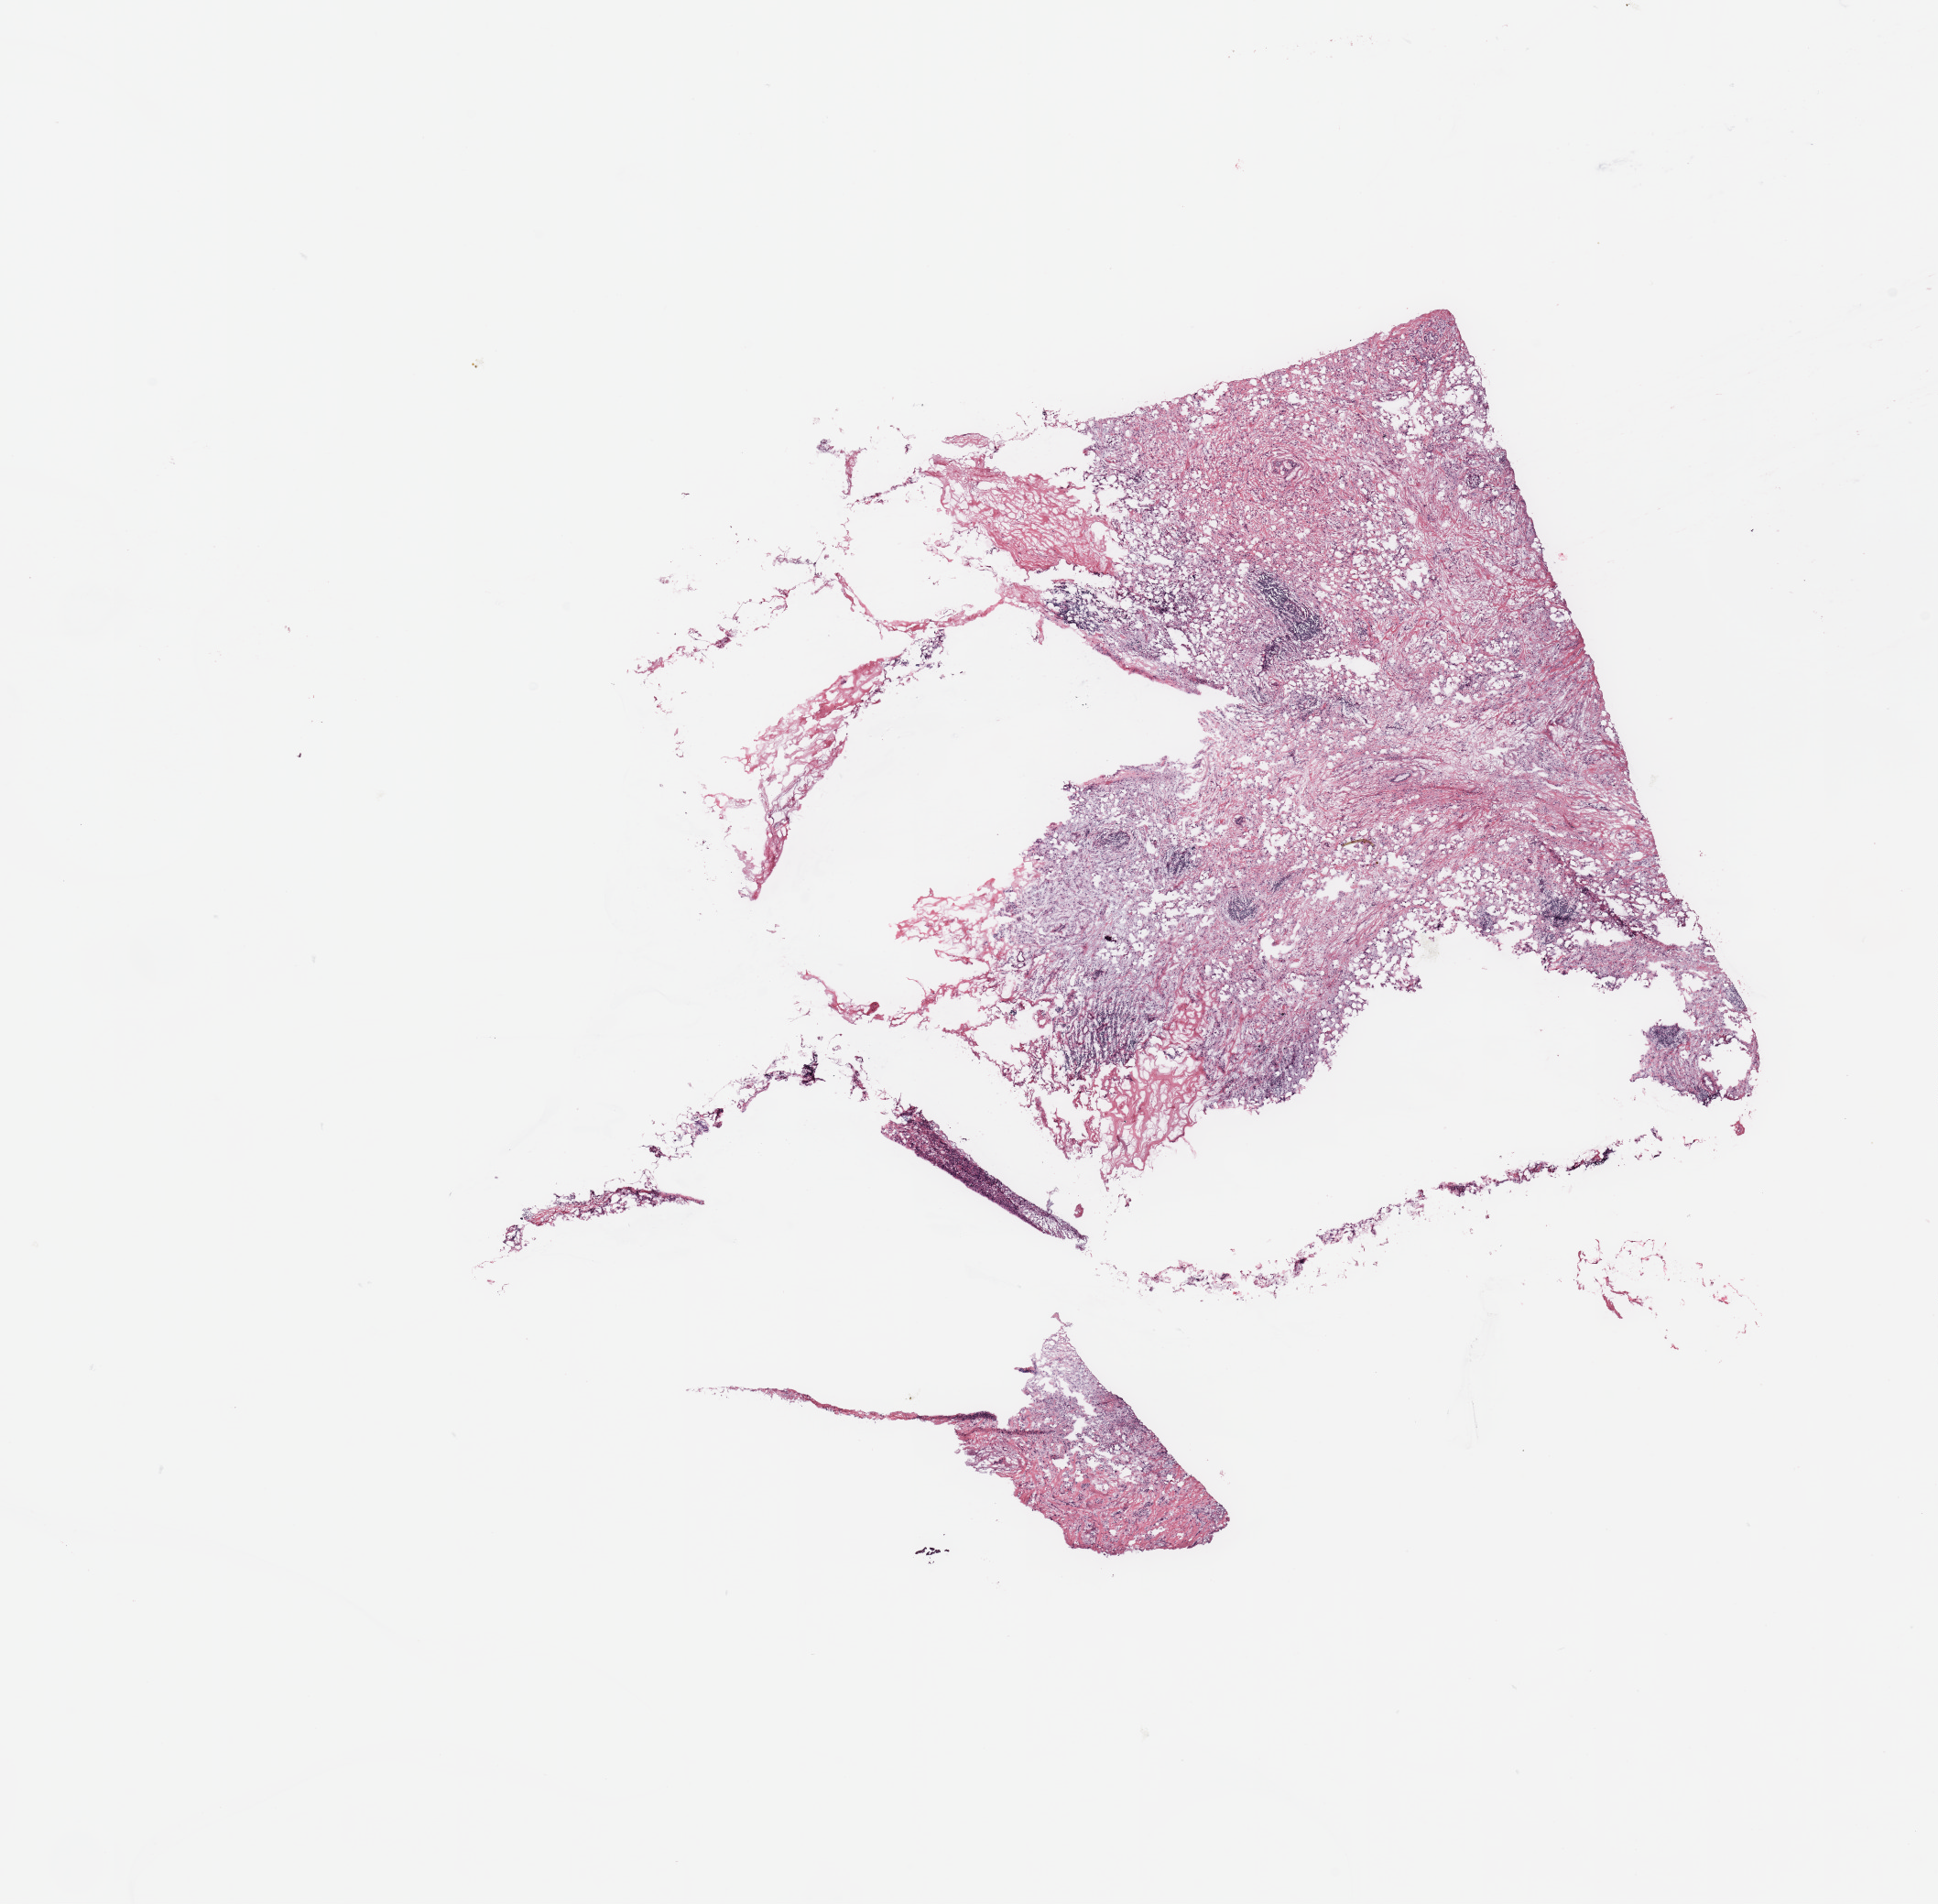
H&E whole-slide image, a low-resolution overview of the entire scanned area, about 16.7 x 16.4 mm (from a 20x scan); tumour tissue sample, breast. Female, 74 y/o.
Diagnosis: Infiltrating duct carcinoma, NOS. AJCC pathologic stage: IIA.